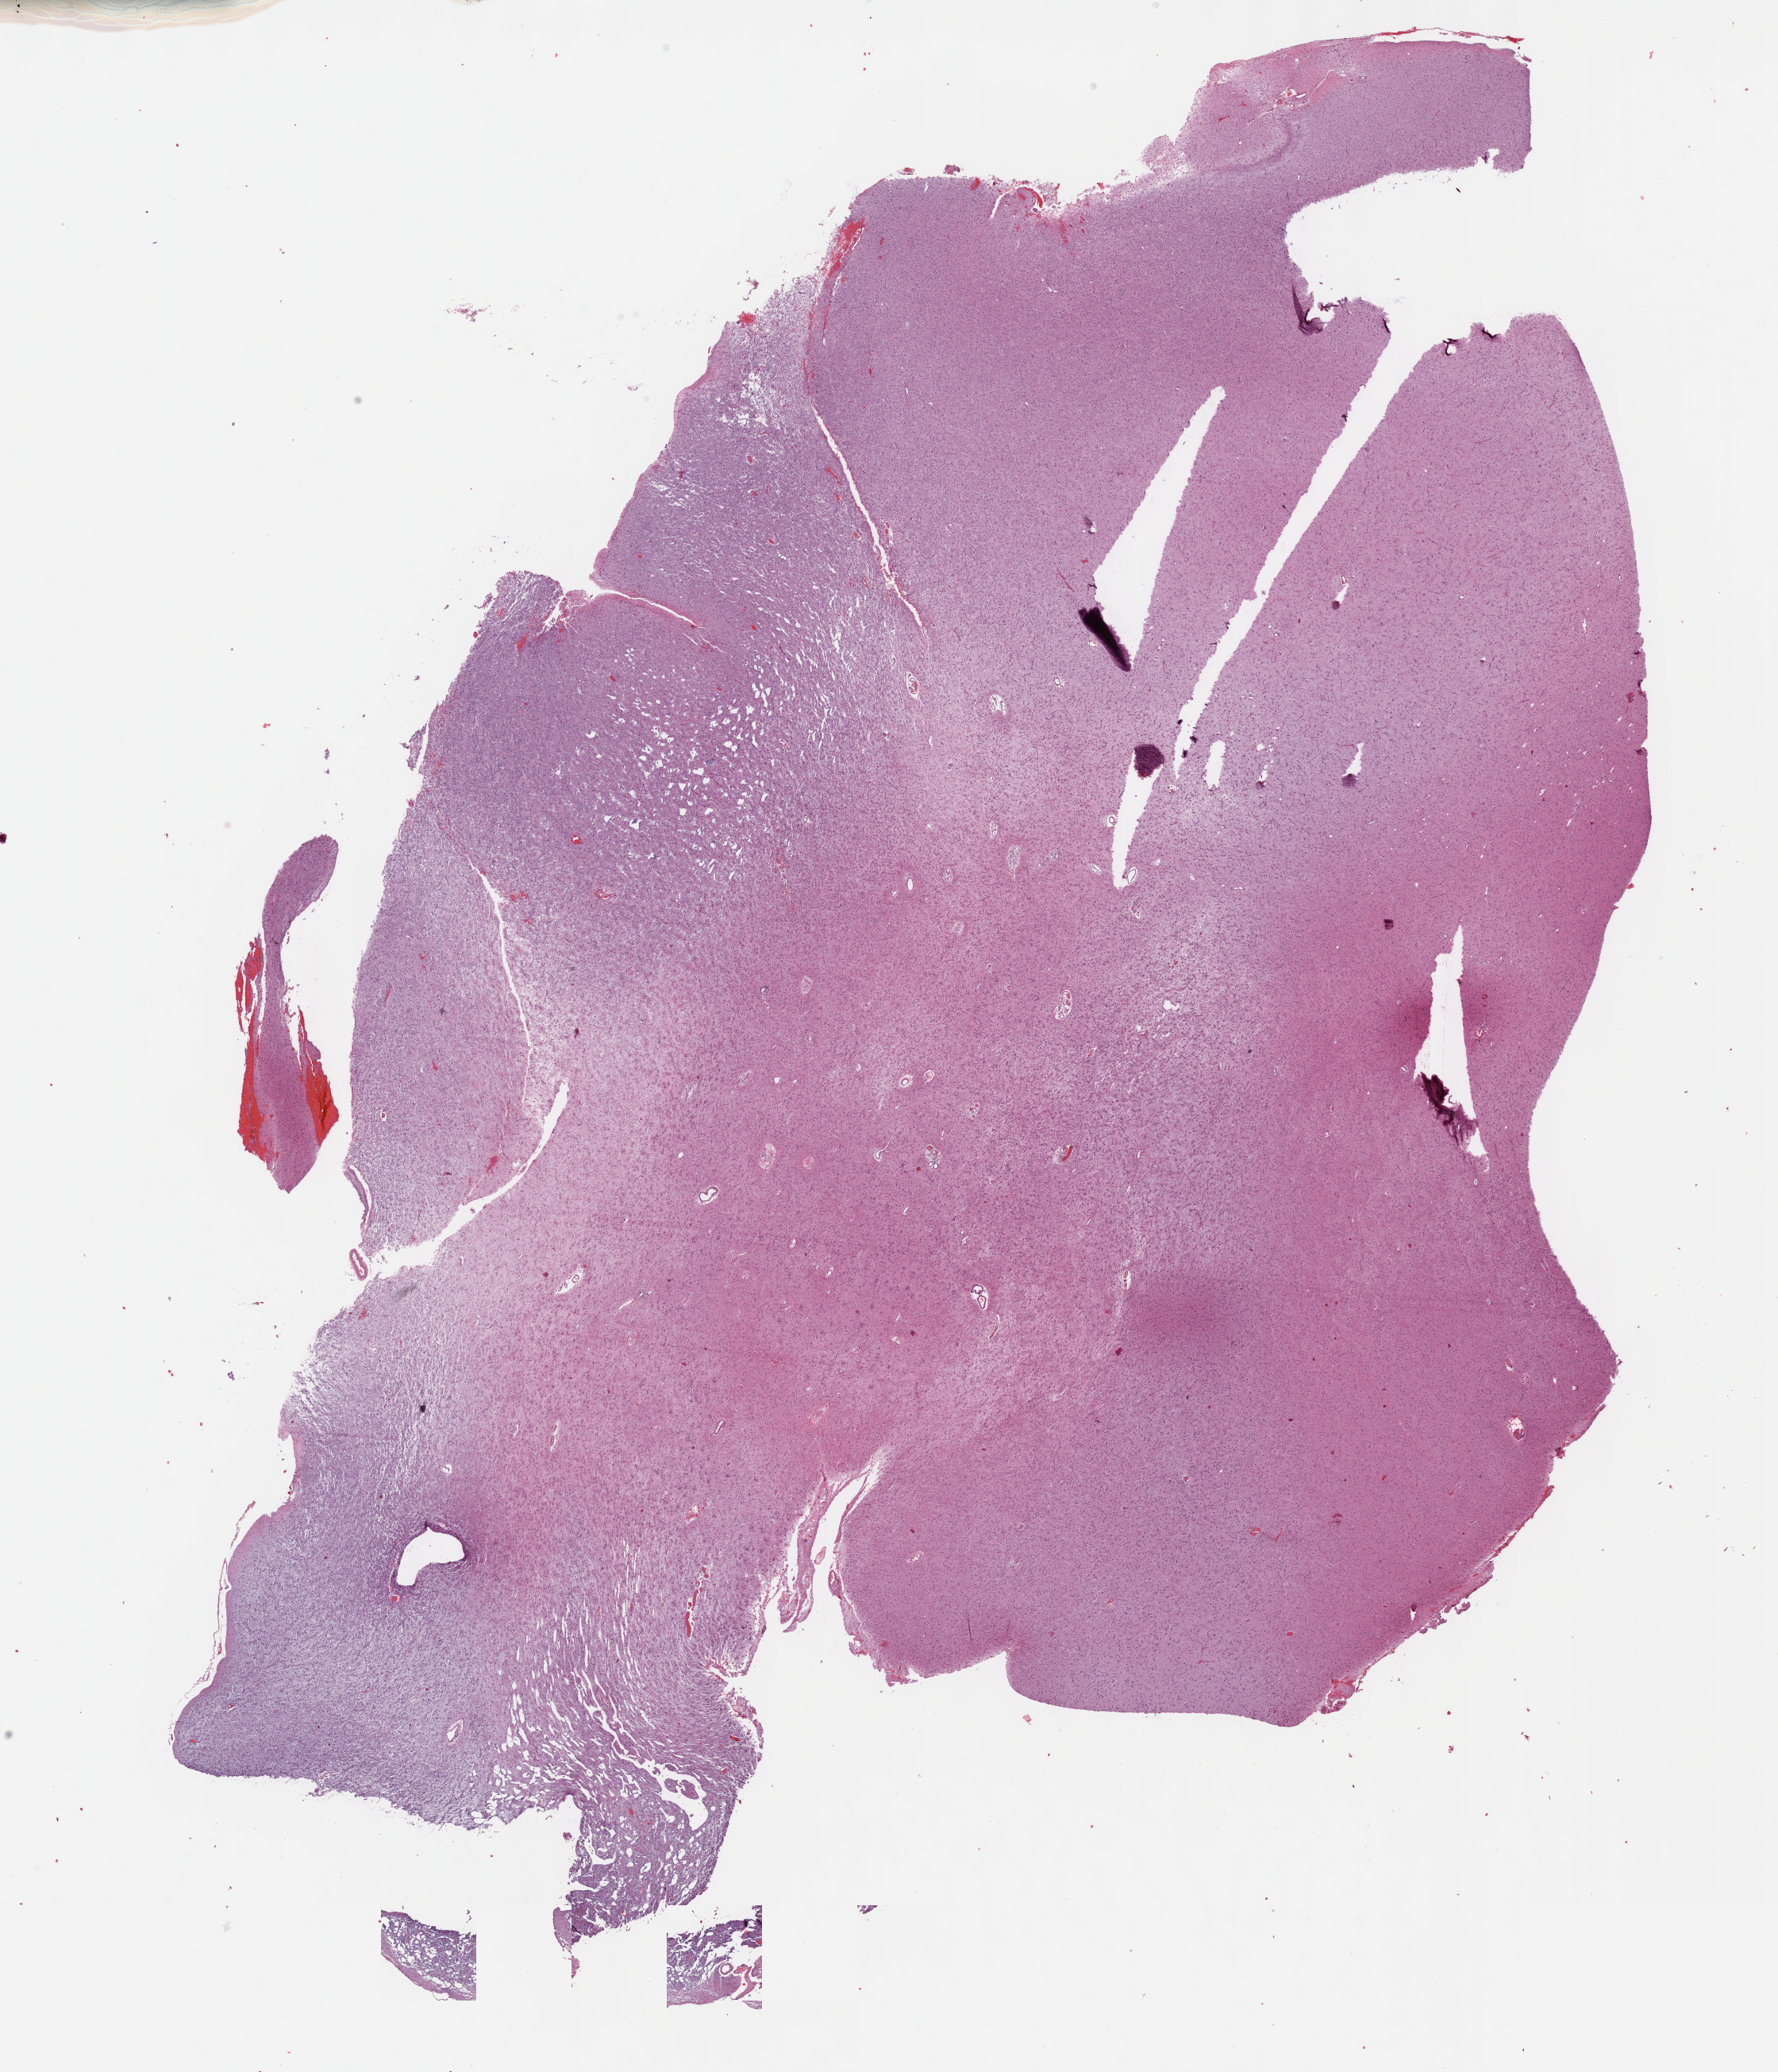
Digitized Hematoxylin and eosin (H&E) stained tissue section (whole slide) — a low-resolution overview of the entire scanned area, about 18.1 x 21.1 mm (acquisition: 40x scan). Formalin-fixed paraffin-embedded (FFPE) diagnostic section. Brain, primary tumour sample. Male, age 58 years at initial diagnosis. Histologic grade: G3 (poorly differentiated).
- laterality: left
- histologic diagnosis: Mixed glioma (cerebrum)